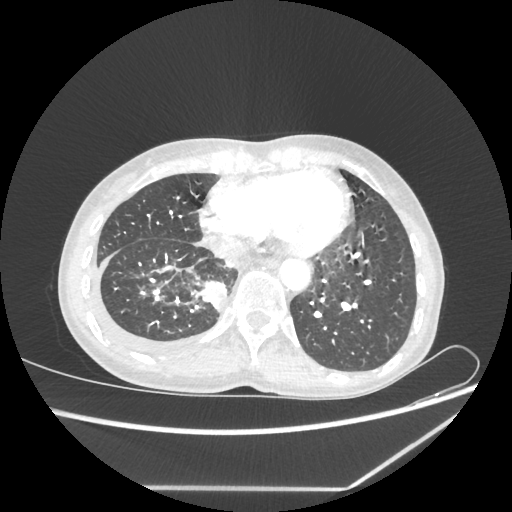
Chest CT, one axial slice. Position 69 of 237 along the scan axis. Reconstruction kernel STANDARD. 80 kVp. Lung window (W 1500 / L -600 HU). 512 × 512 image matrix, field of view 364 × 364 mm. Female patient, age 59 years. From the clinical record (not read from this slice): clinical TNM (as recorded): T1c N1 M1.
Annotated regions visible in this slice (bounding box drawn by a radiologist):
- lung tumour (recorded histology: adenocarcinoma): bounding box <198,279,231,312> (left, top, right, bottom; pixels)